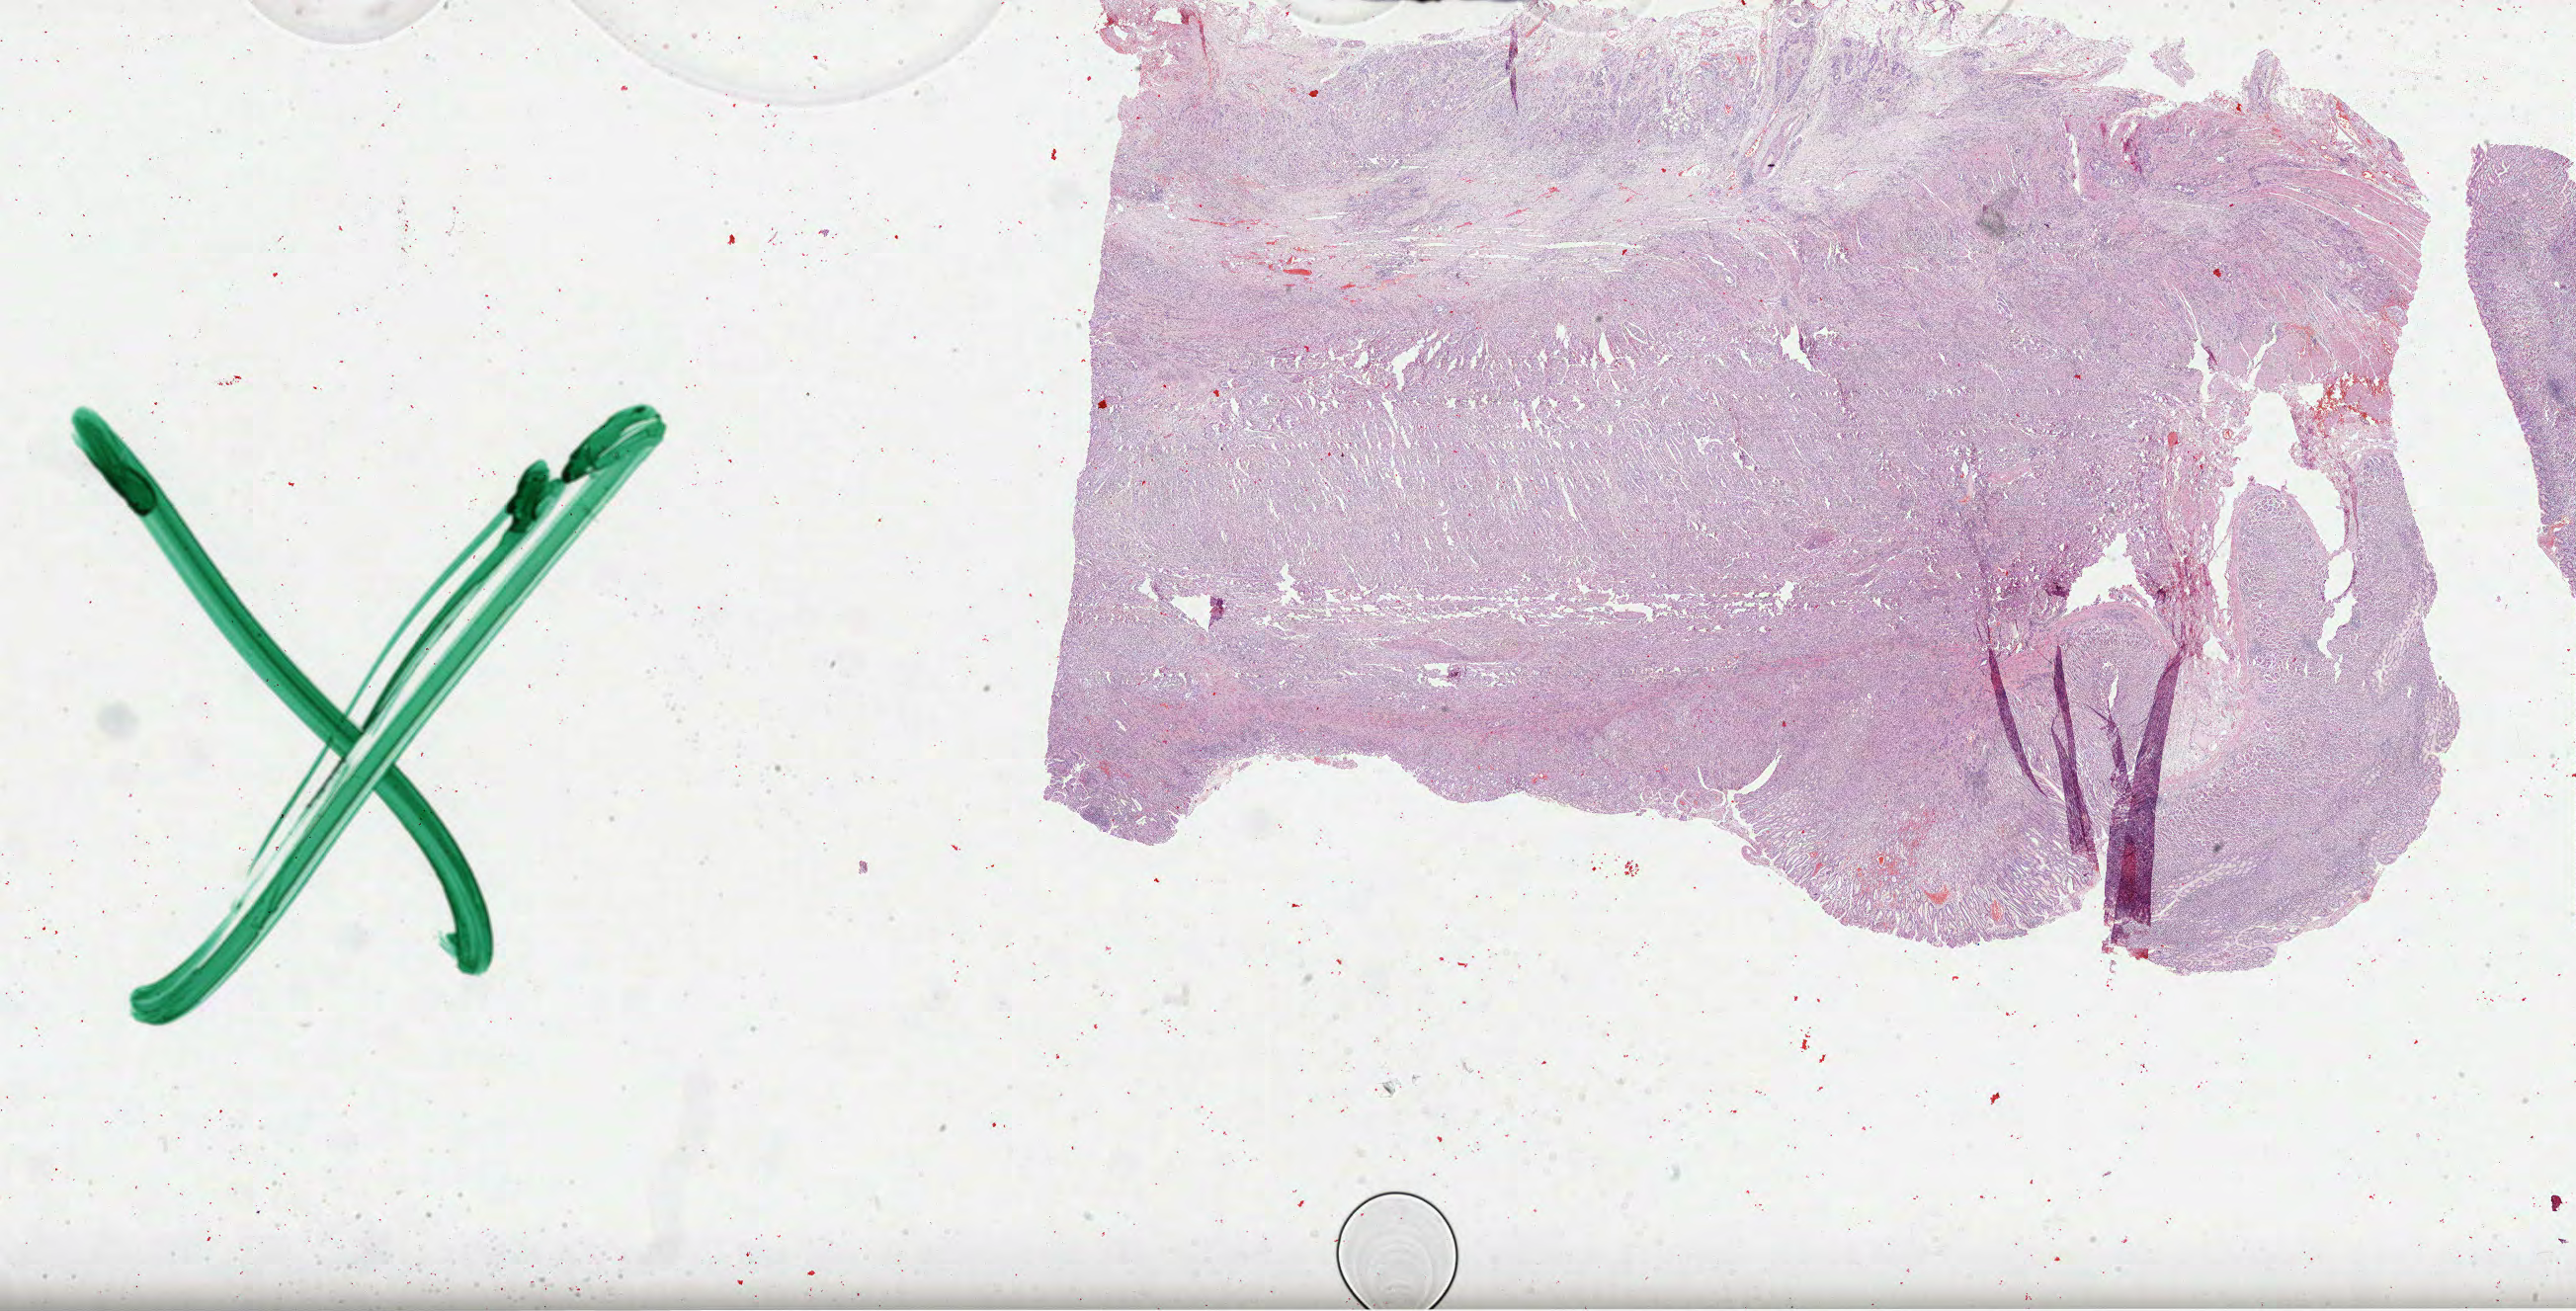
Whole-slide histology image, H&E — whole scanned area (about 42.1 x 21.4 mm) shown as a low-resolution overview, formalin-fixed paraffin-embedded (FFPE) diagnostic section, primary tumour sample from the stomach. Male patient; age at initial diagnosis 58 years. Histologic grade: G3 (poorly differentiated).
Diagnosis: Carcinoma, diffuse type (cardia, NOS). Lymph nodes positive (case pathology): 6 of 9 examined. AJCC pathologic stage: IIIA (6th edition).